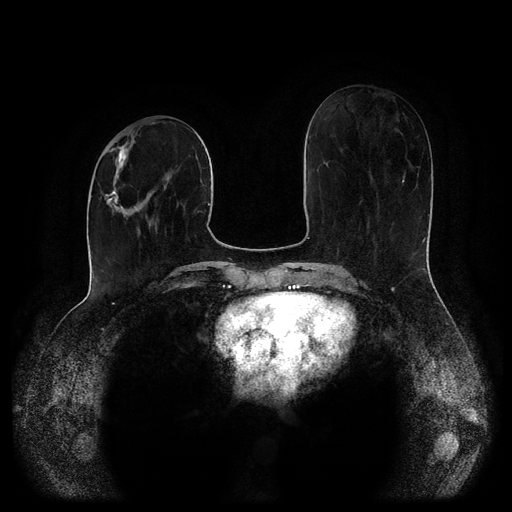
Breast MRI (dynamic contrast-enhanced, multi-phase), one axial slice; position 39 of 116 along the scan axis; dynamic contrast-enhanced series, time point 2 of 5 at this slice position (early post-contrast); 1.5 T; TE 2.6 ms, TR 5.2 ms; 2 mm slice thickness; 512 × 512 image matrix, field of view 380 × 380 mm. Patient: female, 52 years.
Annotated regions visible in this slice (semi-automatic segmentation, software-assisted and operator-edited):
- breast lesion (labelled 'tumour' in the annotation; benign lesions carry a separate 'benign' label): bounding box (x1, y1, x2, y2) in pixels: (100, 142, 130, 220)